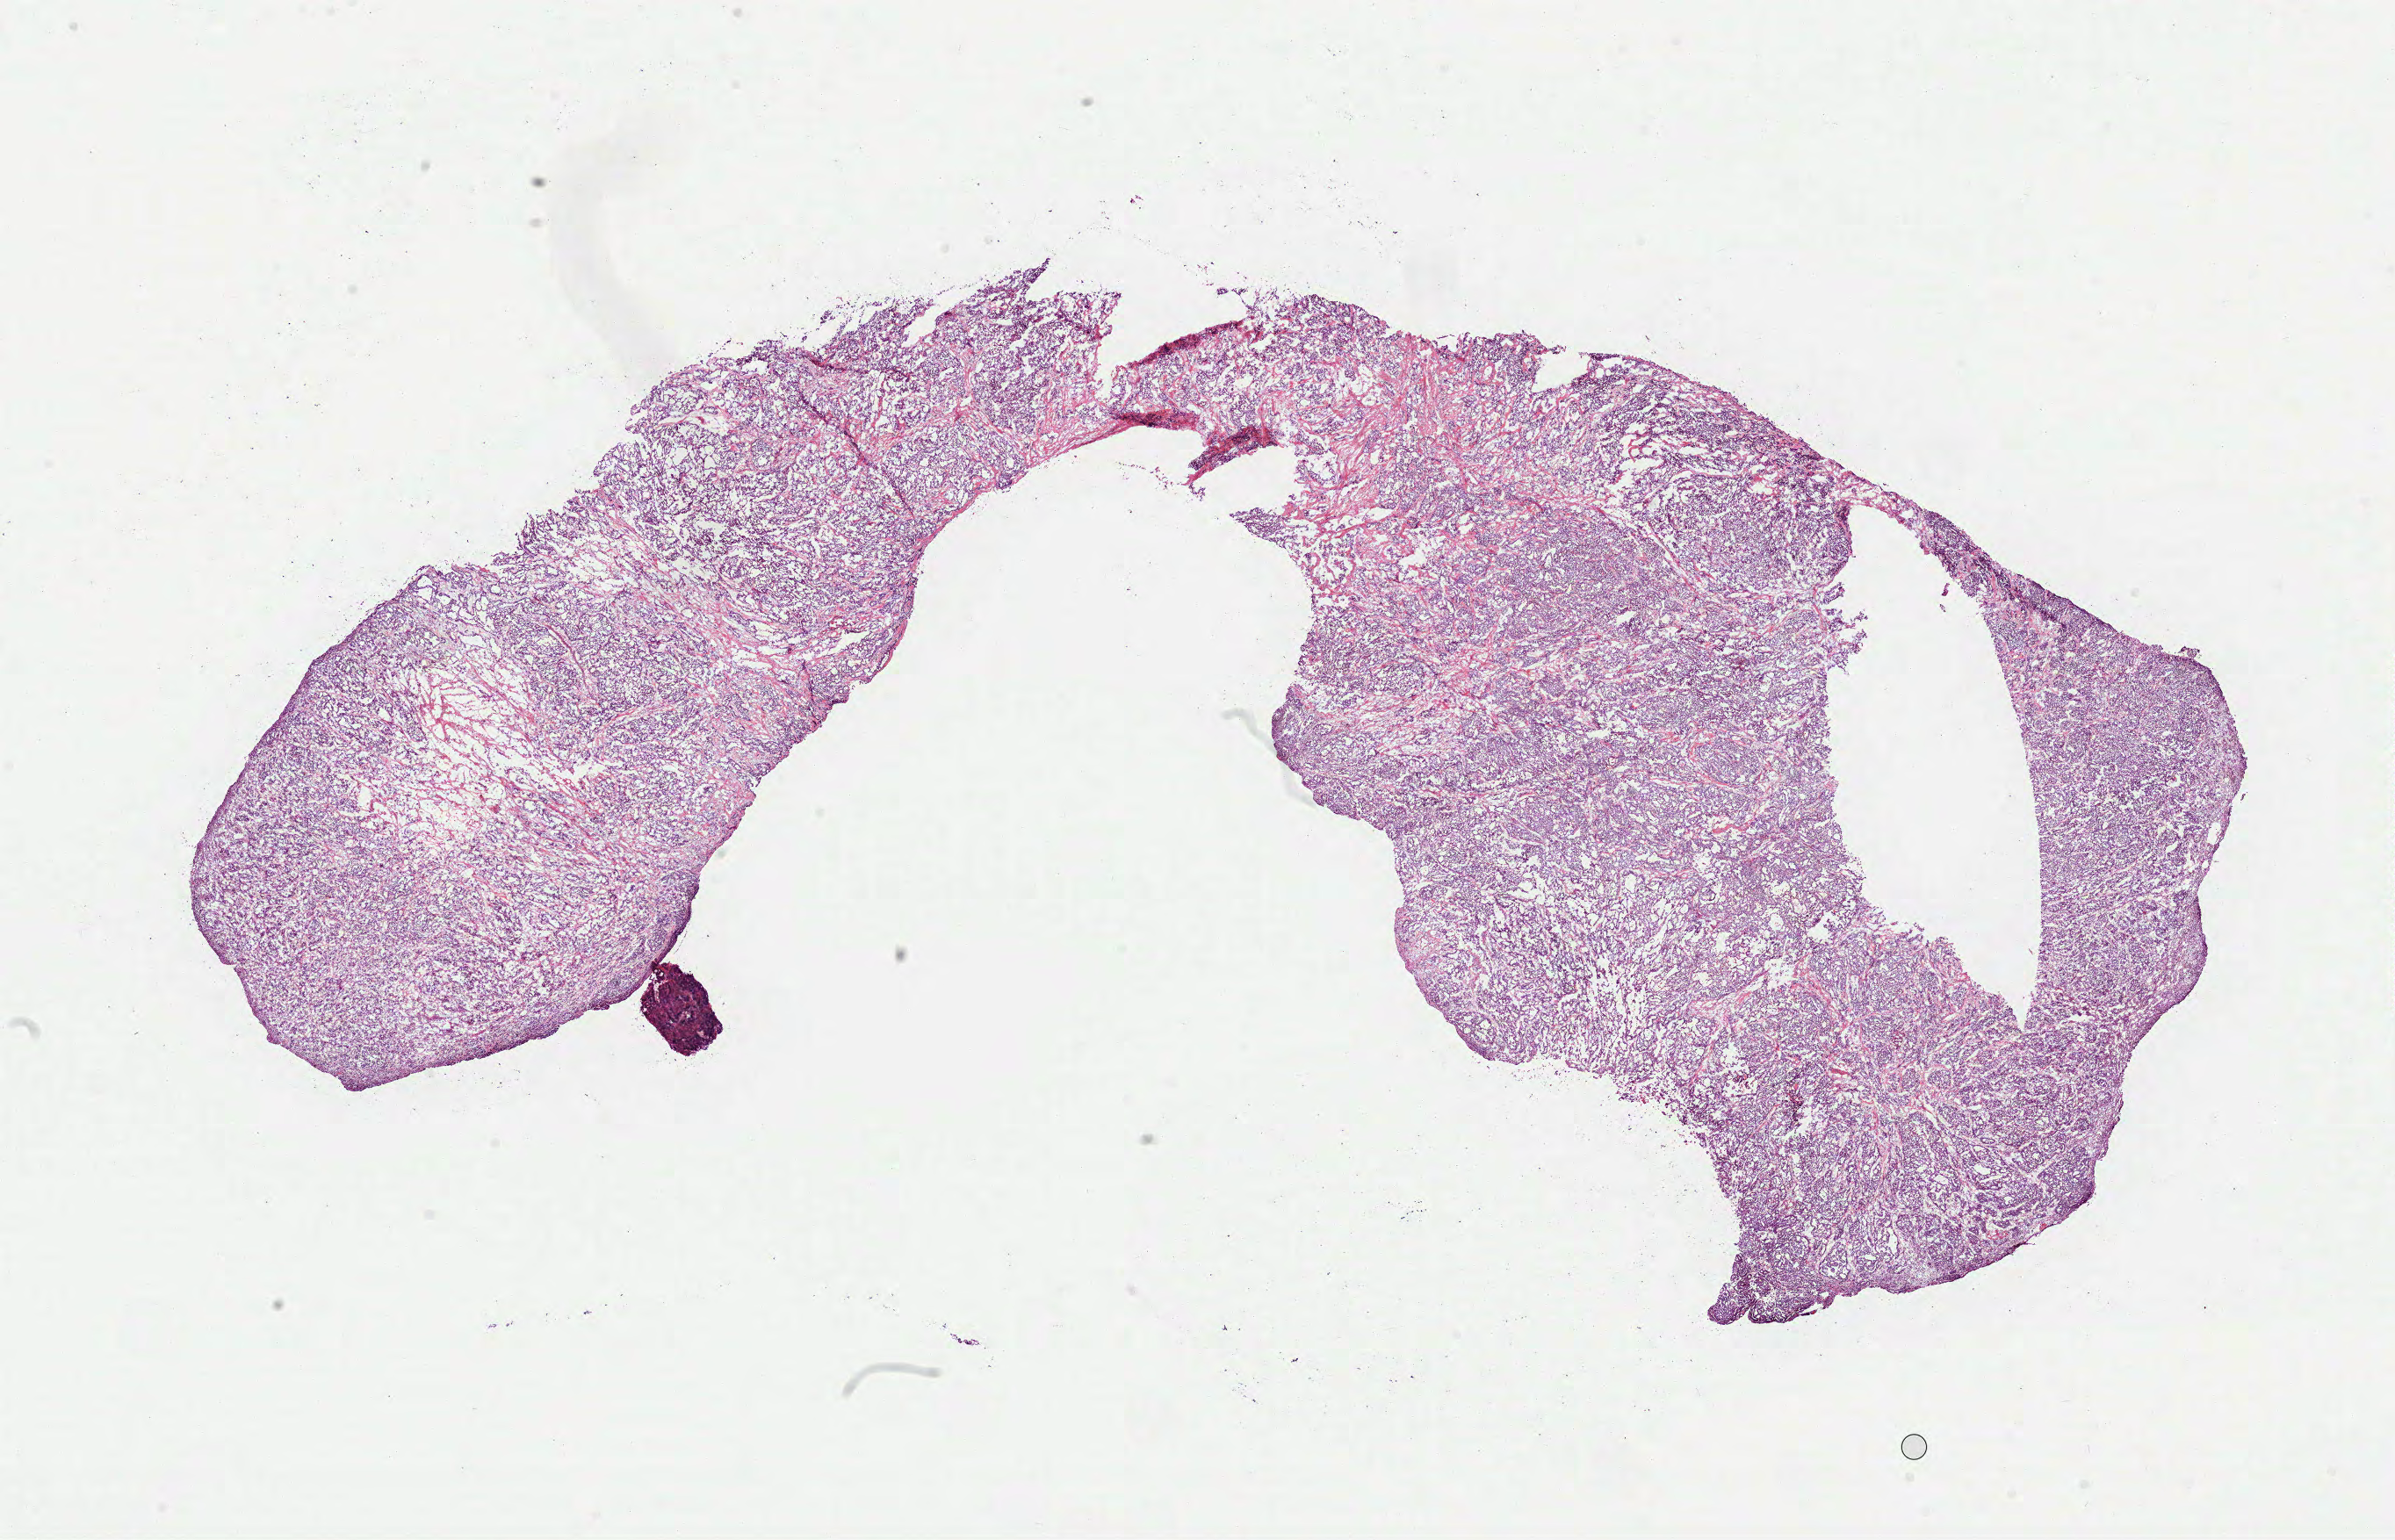
Digitized H&E-stained tissue section (whole slide) — a low-resolution overview of the entire scanned area, about 22.0 x 14.1 mm (slide scanned at 40x). Frozen section. Lung, recurrent tumour sample. Male patient; age at initial diagnosis 62 years. Slide review estimates, as recorded: tumour cells 99%, tumour nuclei 80%, normal cells 0%, stromal cells 0%, necrosis 1%. Inflammatory infiltration, as recorded: lymphocyte infiltration 5%, monocyte infiltration 0%, neutrophil infiltration 0%.
• this section: recurrent tumour
• patient diagnosis: Adenocarcinoma with mixed subtypes (upper lobe, lung)